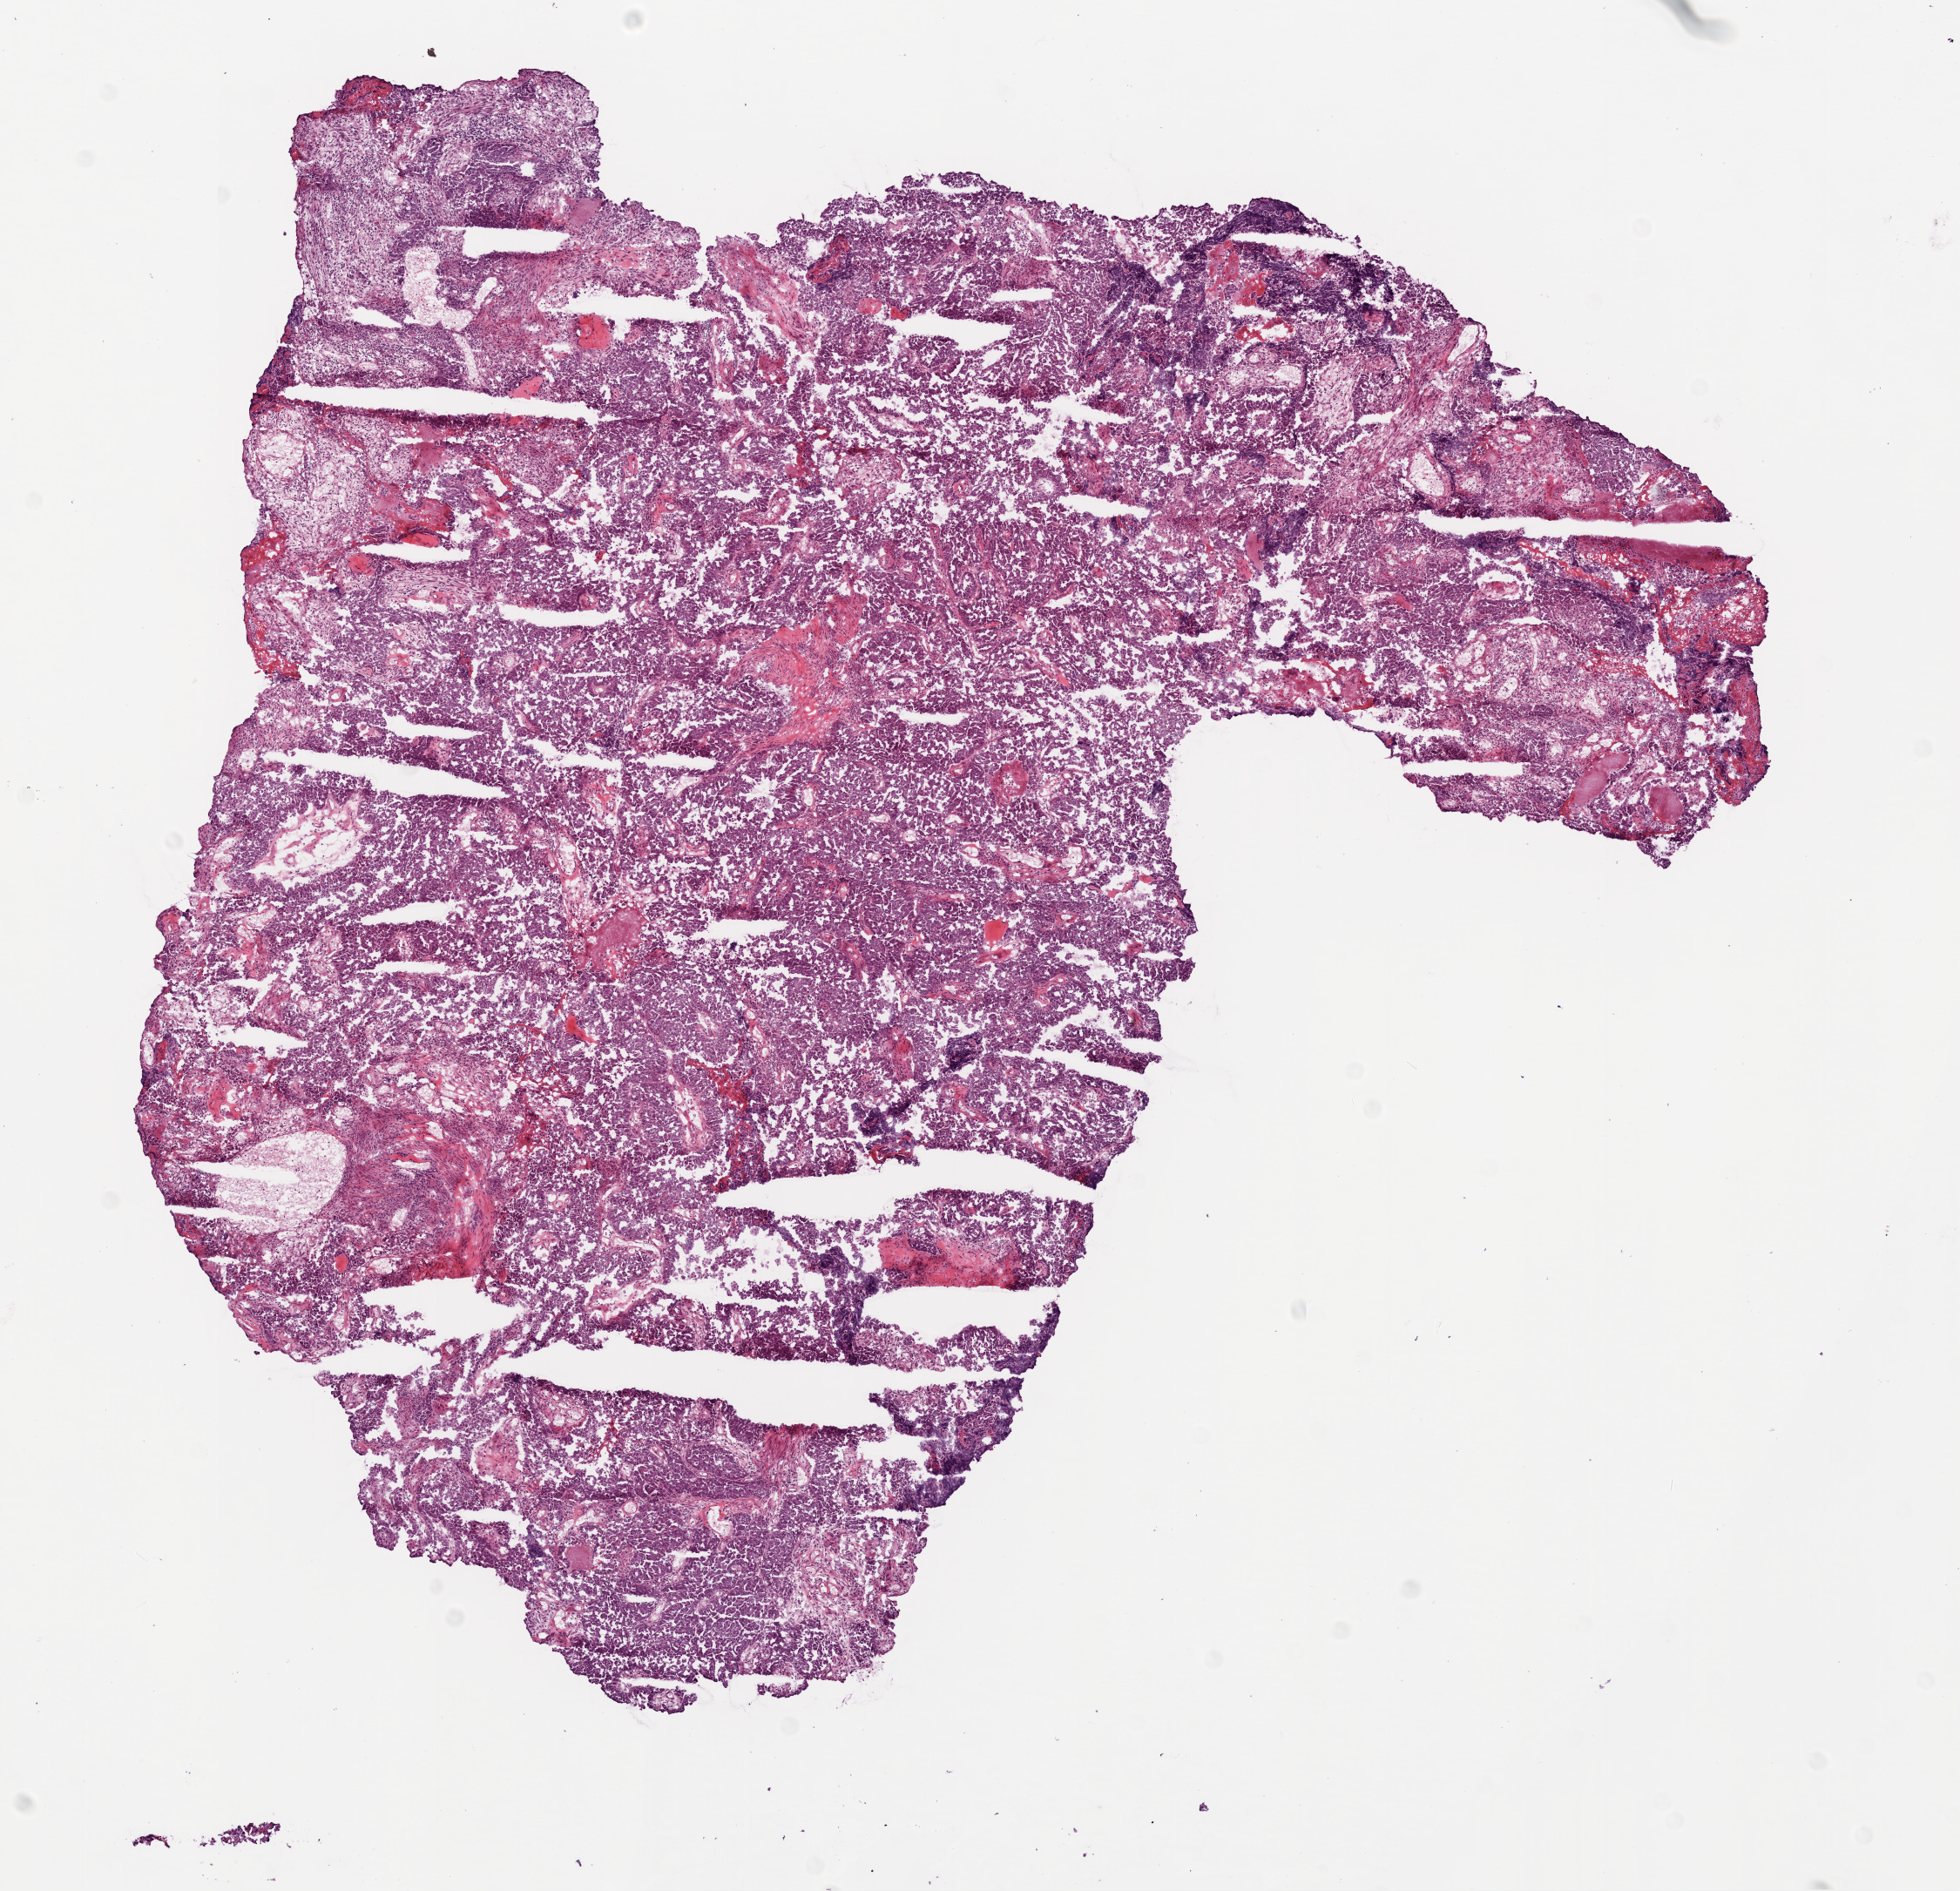
H&E-stained whole-slide image, shown as a low-resolution overview of the whole scanned area (about 9.0 x 8.7 mm), frozen section from the bottom of the tissue portion, primary tumour sample from the ovary. Female, age 57 years at initial diagnosis. Histologic grade: G3 (poorly differentiated). Slide review estimates, as recorded: tumour cells 90%, tumour nuclei 95%, normal cells 0%, stromal cells 5%, necrosis 5%.
Pathologic diagnosis: Serous cystadenocarcinoma, NOS. FIGO stage: IIIC. Laterality: right.